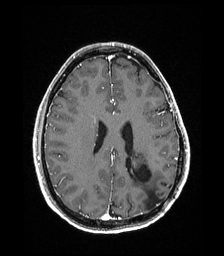
Brain MRI from a brain-tumour surgery series, one axial slice. Position 76 of 192 along the scan axis. T1-weighted post-contrast. 1 mm slice thickness. 224 × 256 image matrix. Case-level facts recorded for this patient, not image findings: histopathology: Low grade glioma; IDH mutation: no.
Annotated regions visible in this slice (manually delineated by an expert):
- previous resection cavity: bounding box <133,164,162,207> (left, top, right, bottom; pixels)
- tumour: <130,153,145,169>